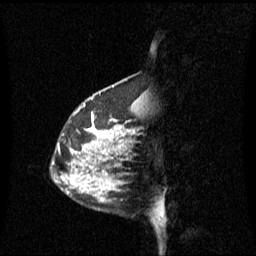
Breast MRI (dynamic contrast-enhanced), one sagittal slice. Slice 20 of 60 in the series (ordered by position). Dynamic contrast-enhanced series, image 2 of 3 at this slice position (ordered by acquisition). 1.5 T. TE 4.2 ms, TR 8.4 ms. 256 × 256 image matrix. Female patient, age 42 years. From the clinical record (not read from this slice): setting: breast cancer imaged before/during neoadjuvant chemotherapy; receptor status: HR-positive, HER2-negative.
Structures marked on this image (semi-automatically segmented with operator editing):
- analysis volume of interest (the breast-tissue region the enhancement analysis was run in; not a lesion): bounding box [x1, y1, x2, y2] px = [68, 100, 137, 201]
- tumour enhancement mask (voxels above the 70 % enhancement threshold inside the analysis volume of interest): [92, 116, 131, 153]